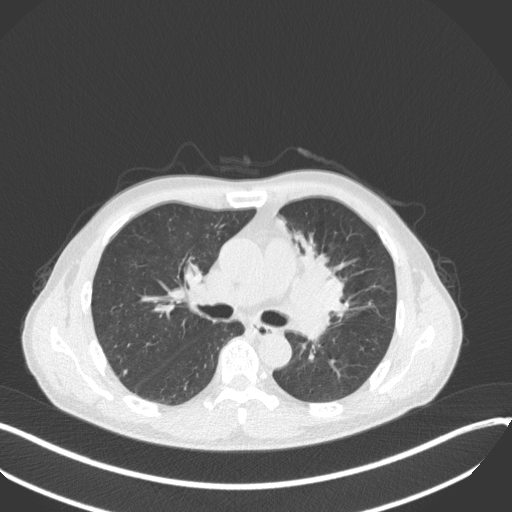
Chest CT, one axial slice; position 202 of 411 along the scan axis; reconstruction kernel B31f; lung window (W 1500 / L -600 HU); 1 mm slice thickness; 512 × 512 image matrix, field of view 400 × 400 mm. Male patient, age 56 years. From the clinical record (not read from this slice): clinical TNM (as recorded): T2a N0 M0.
Annotated regions visible in this slice (rectangle marked by the reading radiologist):
- lung tumour (recorded histology: squamous cell carcinoma): bounding box (x1, y1, x2, y2) in pixels: (290, 232, 356, 332)